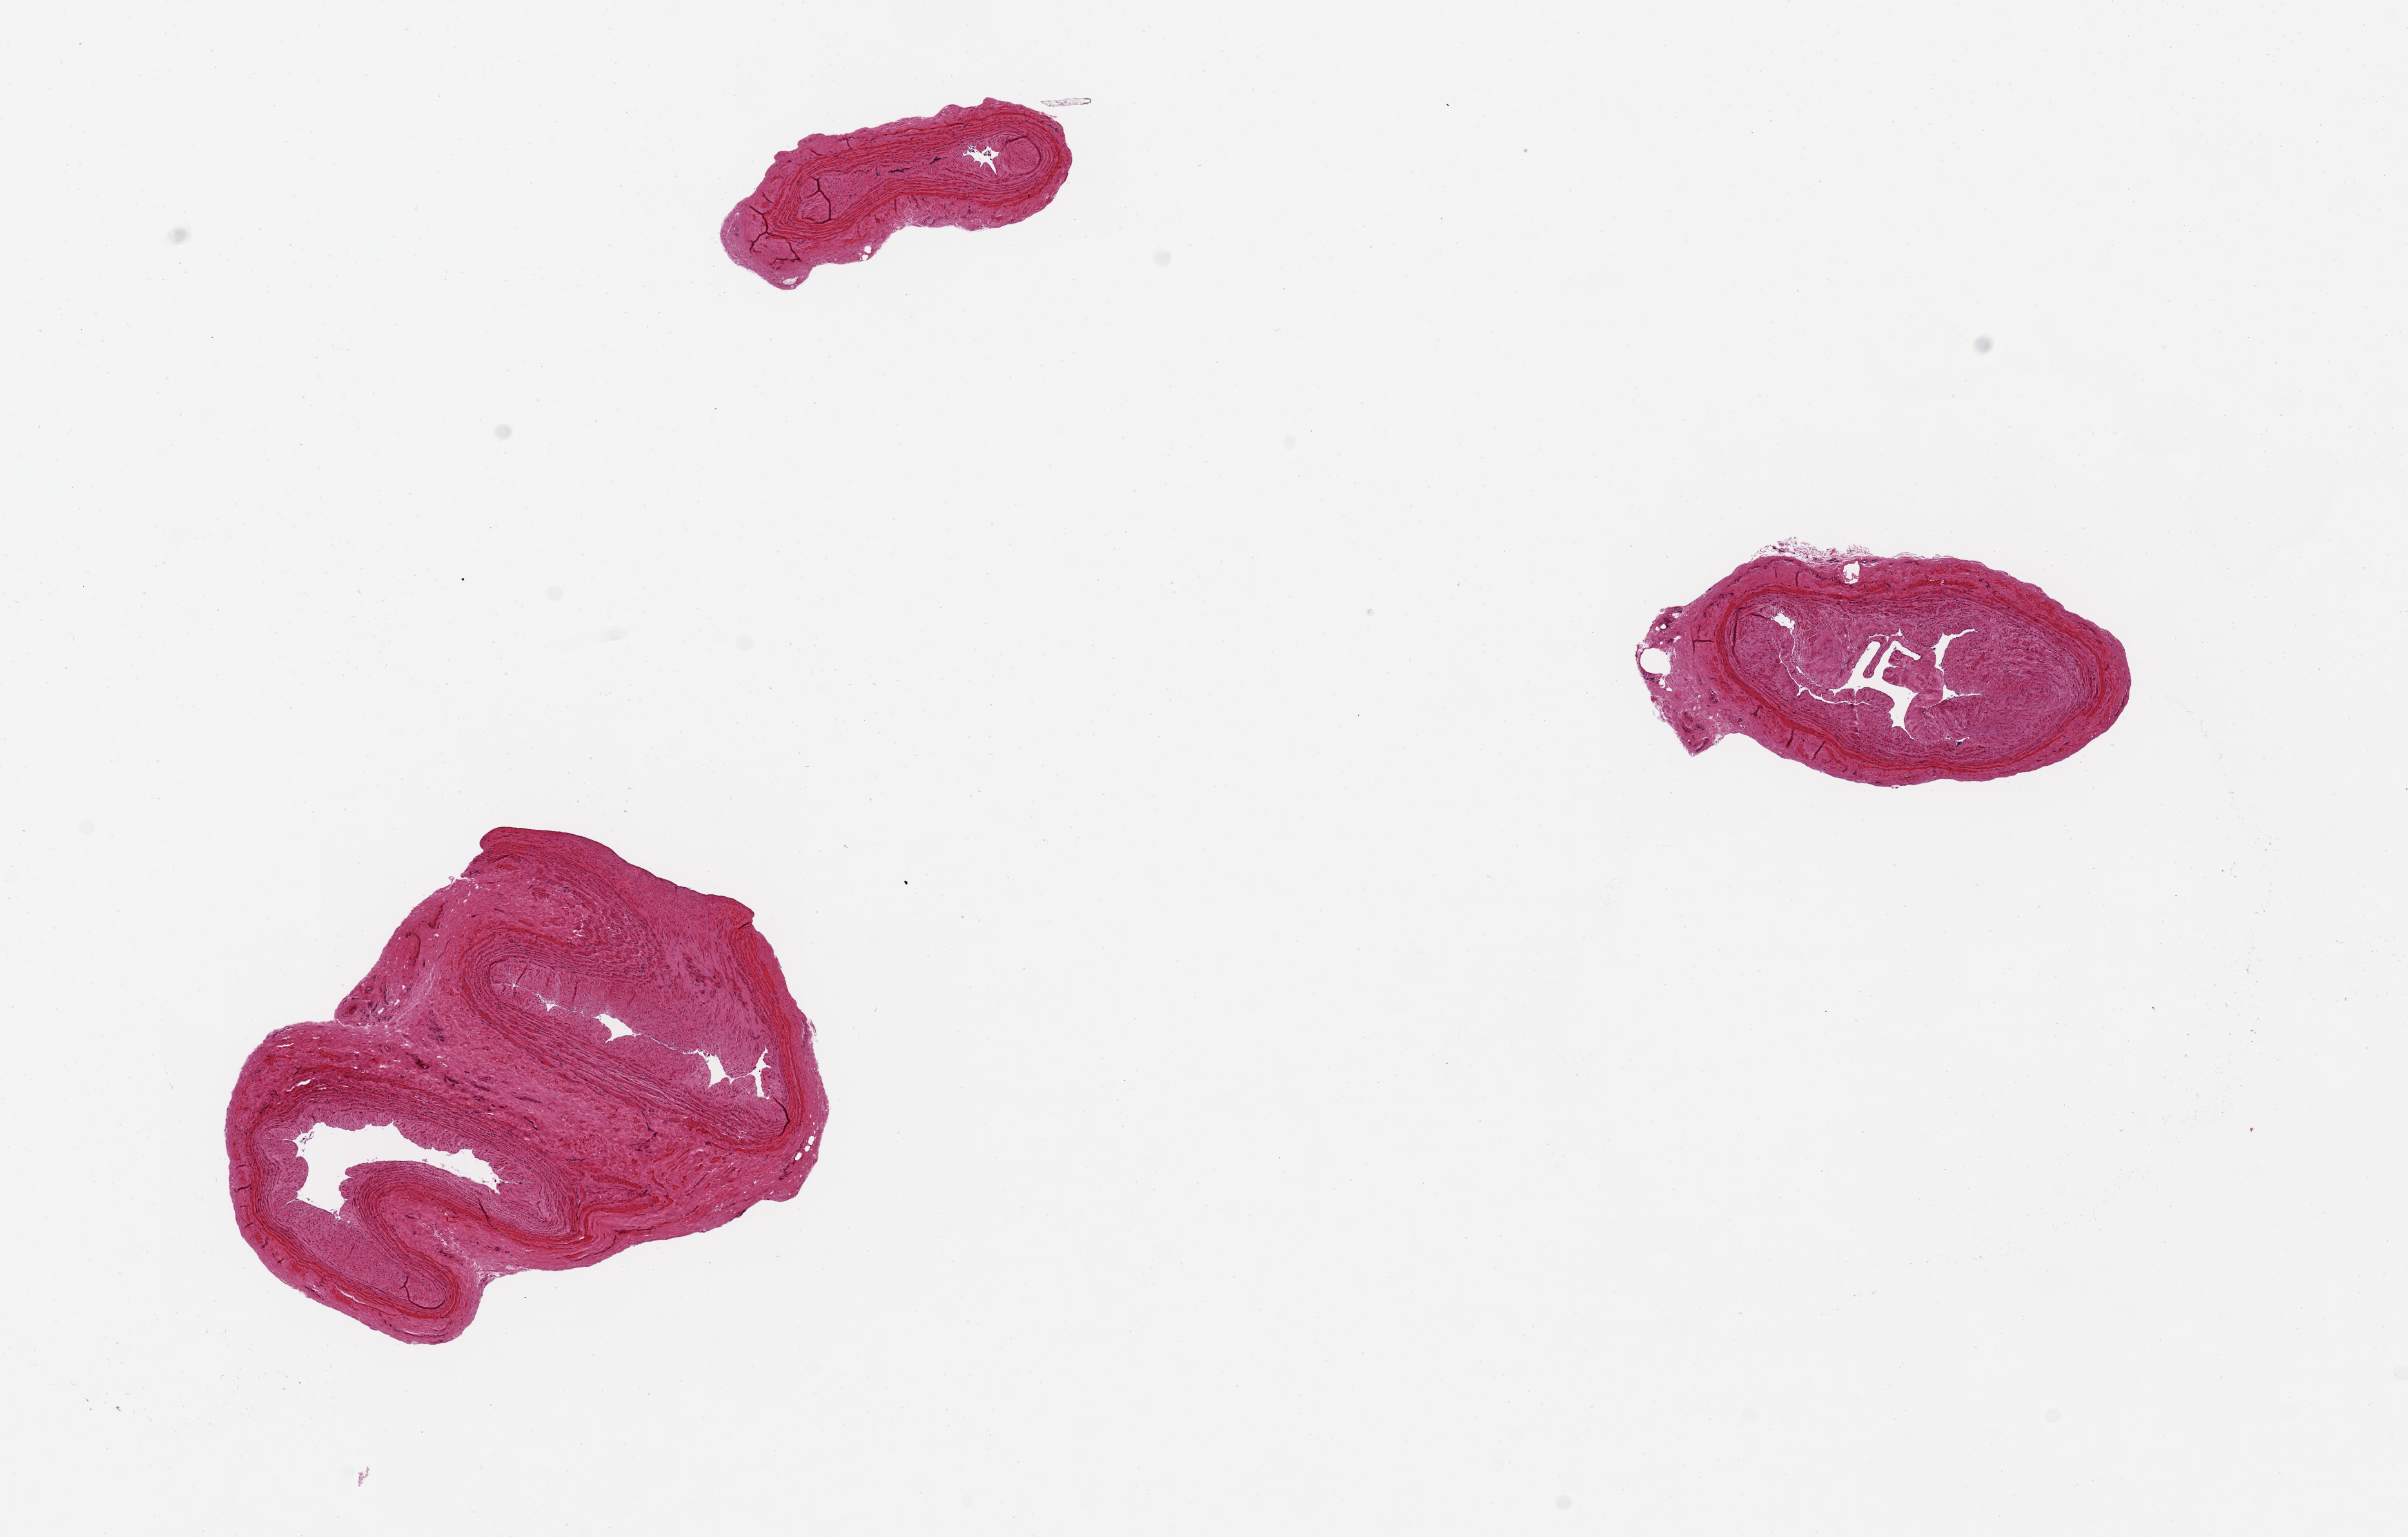
H&E whole-slide image, low-resolution overview of the scanned area, about 14.8 x 9.4 mm. PAXgene-fixed paraffin-embedded (PFPE) section. Sampled site (target tissue): tibial artery. Donor tissue sample. Donor: female.
* reviewer comment on this tissue sample: 2 pieces 3mm, good clean specimens. One addtional small fragment